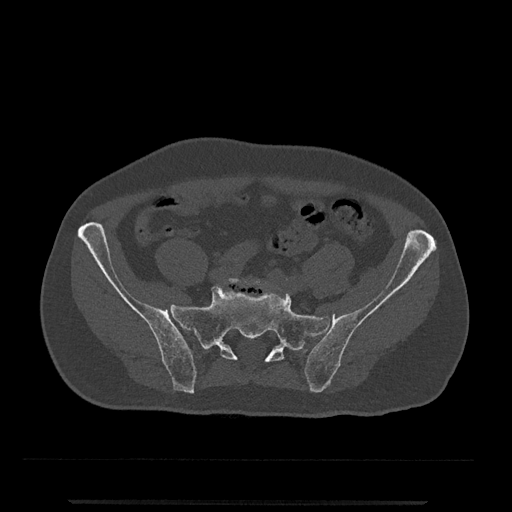
CT including the spine, one axial slice. Slice 13 of 797 in the series (ordered by position). 120 kVp. Bone window (W 1800 / L 400 HU). 0.5 mm slice thickness. 512 × 512 image matrix, field of view 419 × 419 mm. Patient: male, 63 years. From the clinical record (not read from this slice): primary cancer: prostate.
Annotated regions visible in this slice (semi-automatically segmented with operator editing):
- L5 vertebra: bounding box <227,278,268,288> (left, top, right, bottom; pixels)